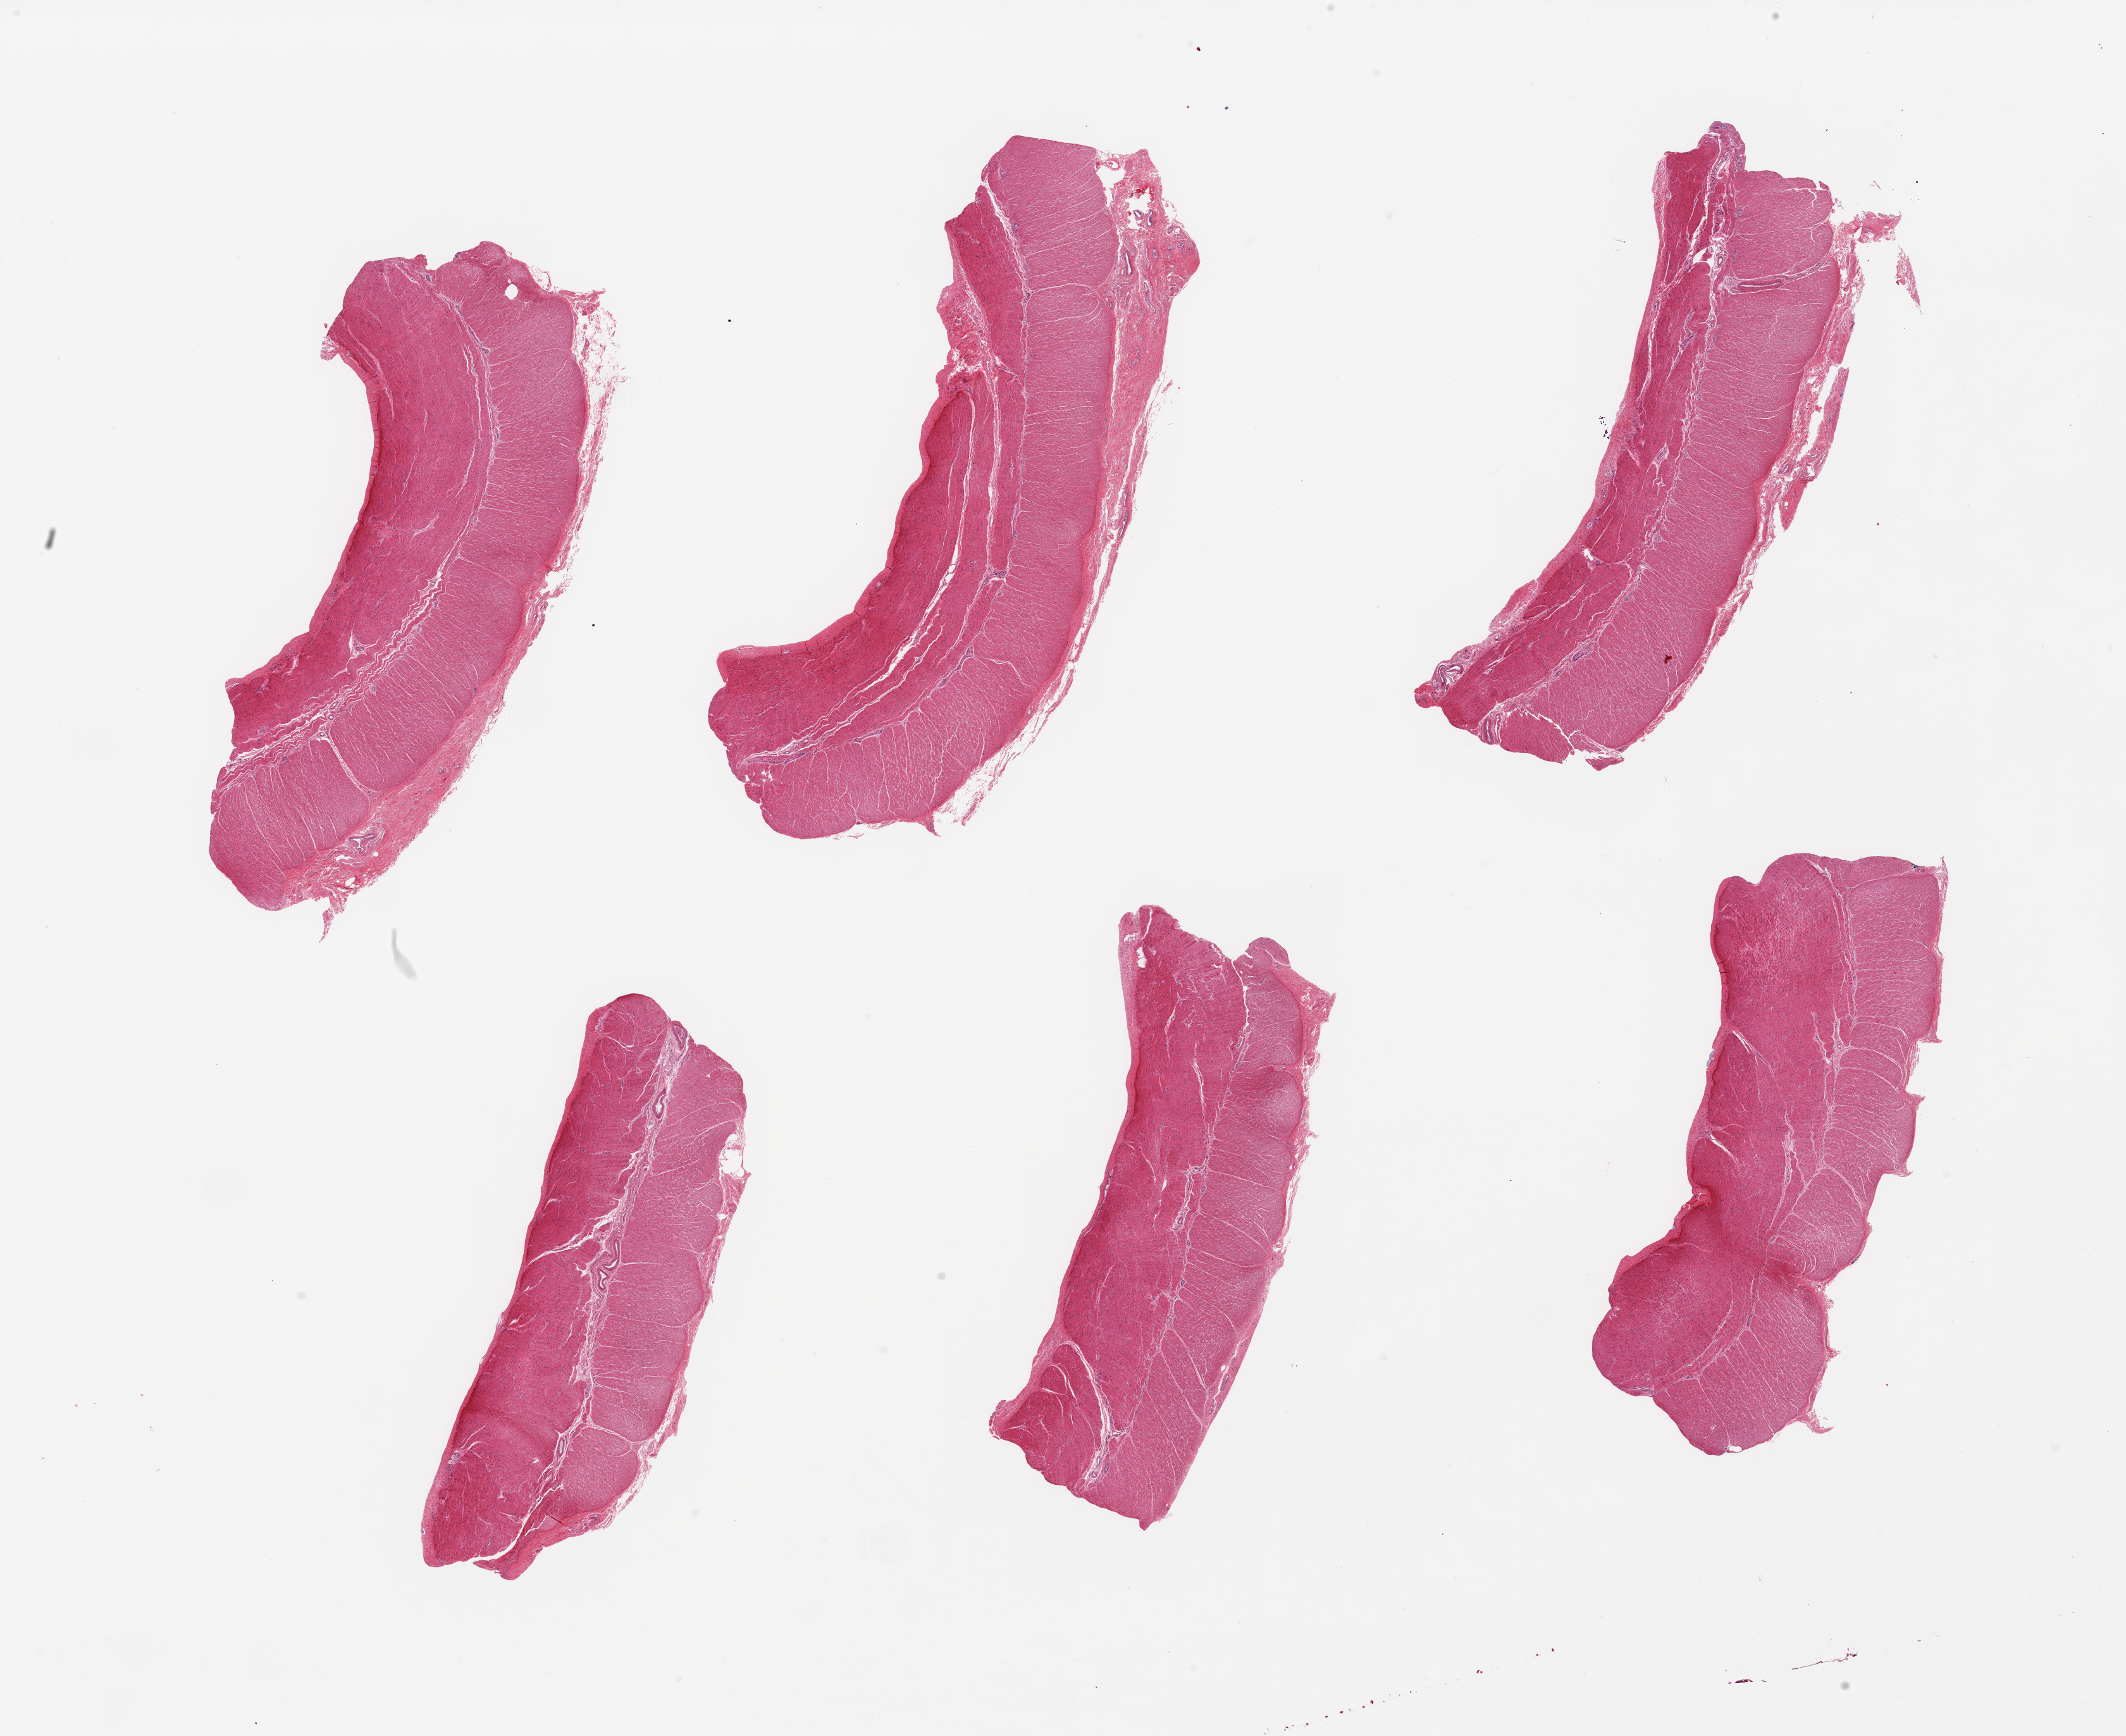
Whole-slide image, haematoxylin and eosin stain, a low-resolution overview of the entire scanned area, about 26.6 x 21.7 mm; PAXgene-fixed paraffin-embedded (PFPE) section; sampled site (target tissue): sigmoid colon; donor tissue sample. Female donor.
- pathologist's review note for this sample: 6 pieces; well trimmed target muscularis